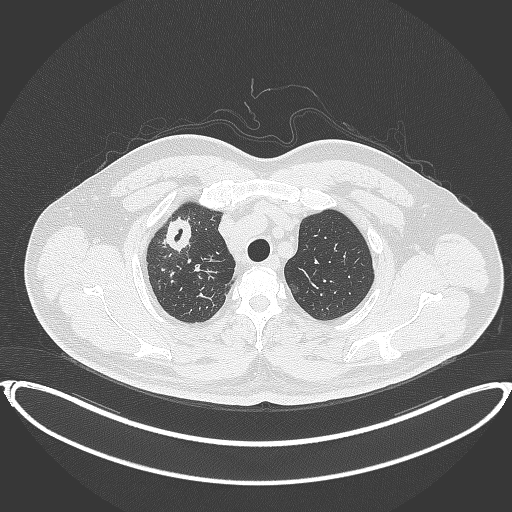
Chest CT, one axial slice; slice 328 of 399 in the series (ordered by position); reconstruction kernel B70f; 120 kVp; lung window (W 1500 / L -600 HU); 1 mm slice thickness; 512 × 512 image matrix. Patient: male, 53 years. Case-level facts recorded for this patient, not image findings: clinical TNM (as recorded): T2a N0 M0.
Outlined on this slice (rectangle marked by the reading radiologist):
- lung tumour (recorded histology: adenocarcinoma): box from (x=164, y=211) to (x=202, y=257) px